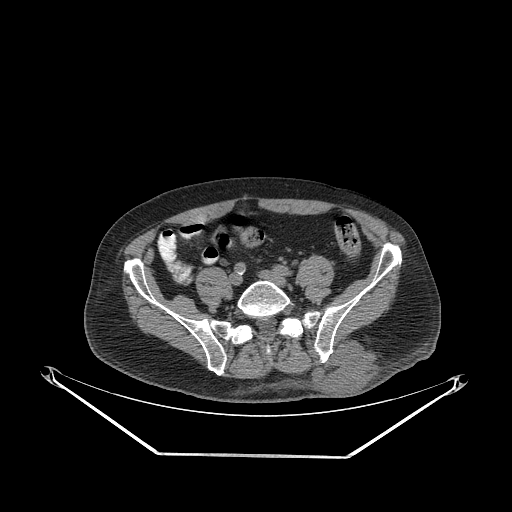
CT of an extremity soft-tissue mass (from a PET/CT study), one axial slice; slice 83 of 267 in the series (ordered by position); reconstruction kernel STANDARD; 140 kVp; soft-tissue window (W 400 / L 40 HU); 3.75 mm slice thickness; 512 × 512 image matrix, field of view 500 × 500 mm. Male patient. Case-level facts recorded for this patient, not image findings: histological type: leiomyosarcoma; grade: intermediate; site of the primary tumour: left pelvis.
Annotated regions visible in this slice (expert contour drawn on MRI and transferred to this co-registered scan by the dataset authors):
- gross tumour volume (mass): bounding box [x1, y1, x2, y2] px = [311, 340, 380, 396]